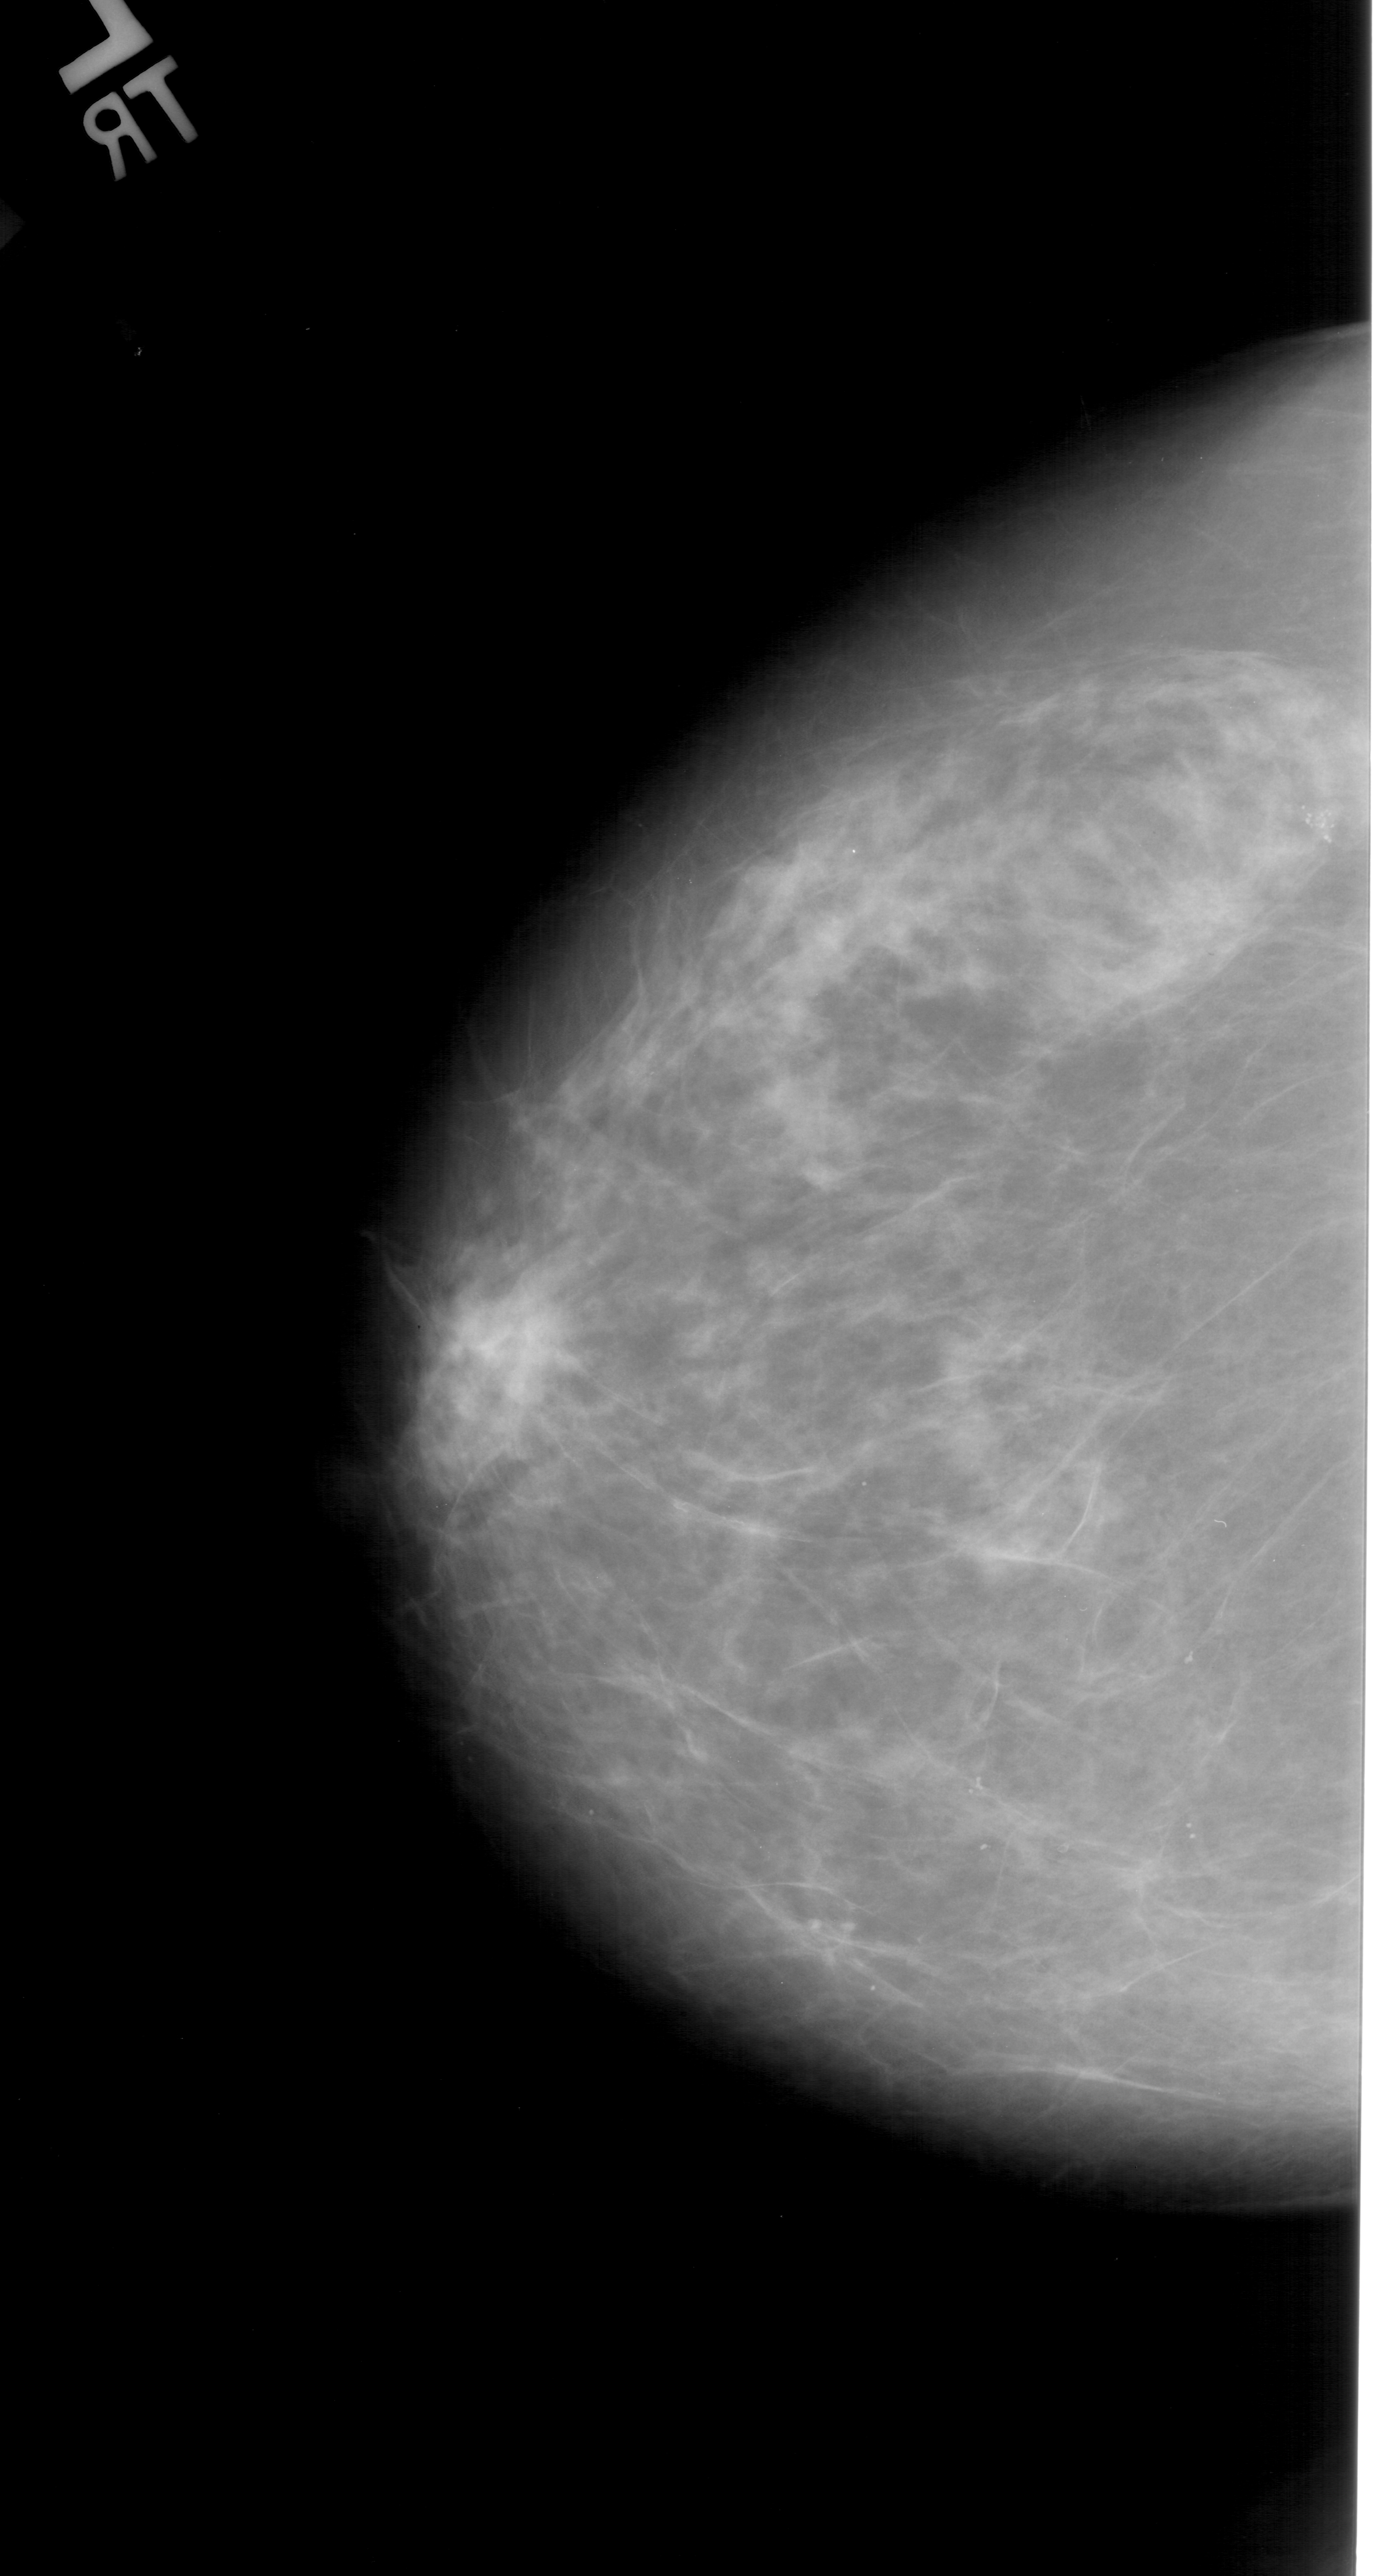
Digitized screen-film mammogram; left breast; CC view.
Marked abnormality: calcifications, morphology pleomorphic, distribution clustered; BI-RADS assessment category 4; subtlety rating 4 on a 1 (subtle) to 5 (obvious) scale; pathology (as recorded): malignant.